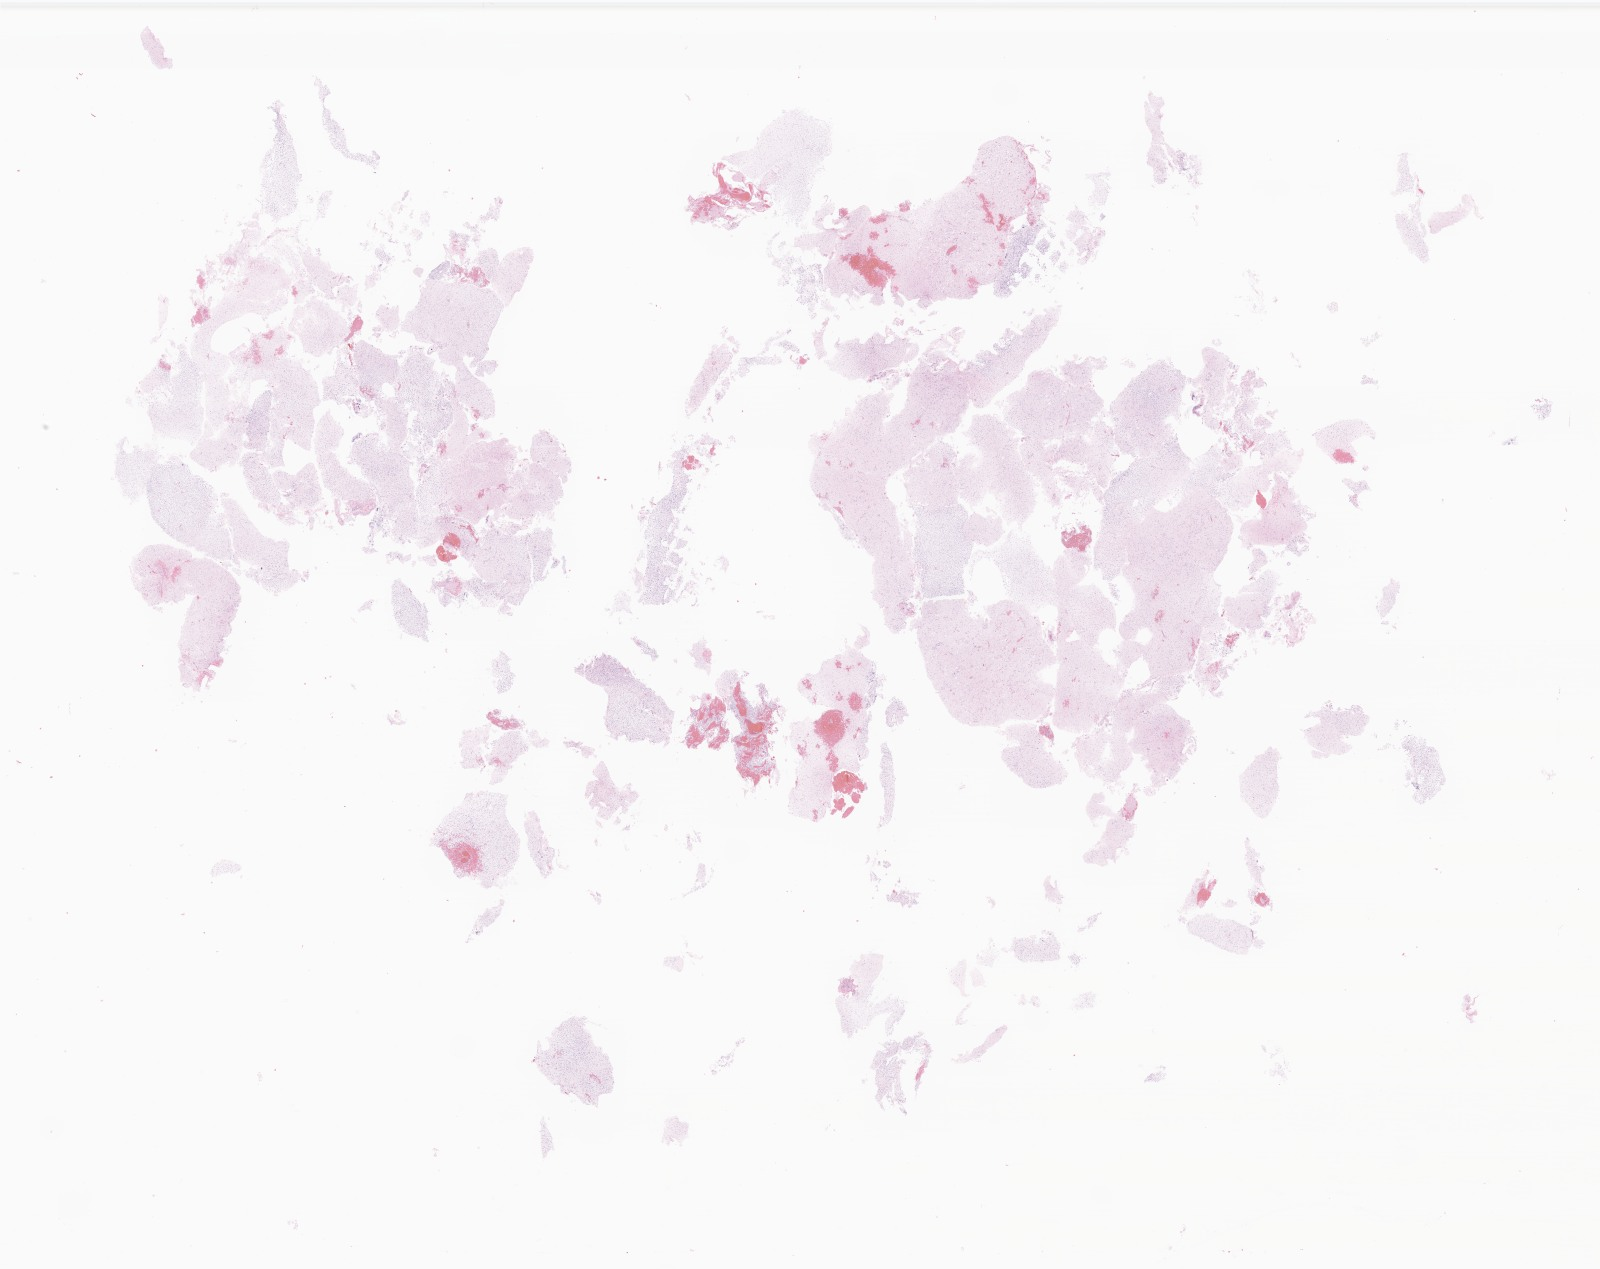
H&E whole-slide image of tumor tissue from the spinal cord, whole scanned area (about 27.0 x 21.4 mm) shown as a low-resolution overview. Formalin-fixed paraffin-embedded section. Patient male; age 63 months (5 years 3 months).
Diagnosis (ICD-O-3 morphology term): Pilocytic astrocytoma.